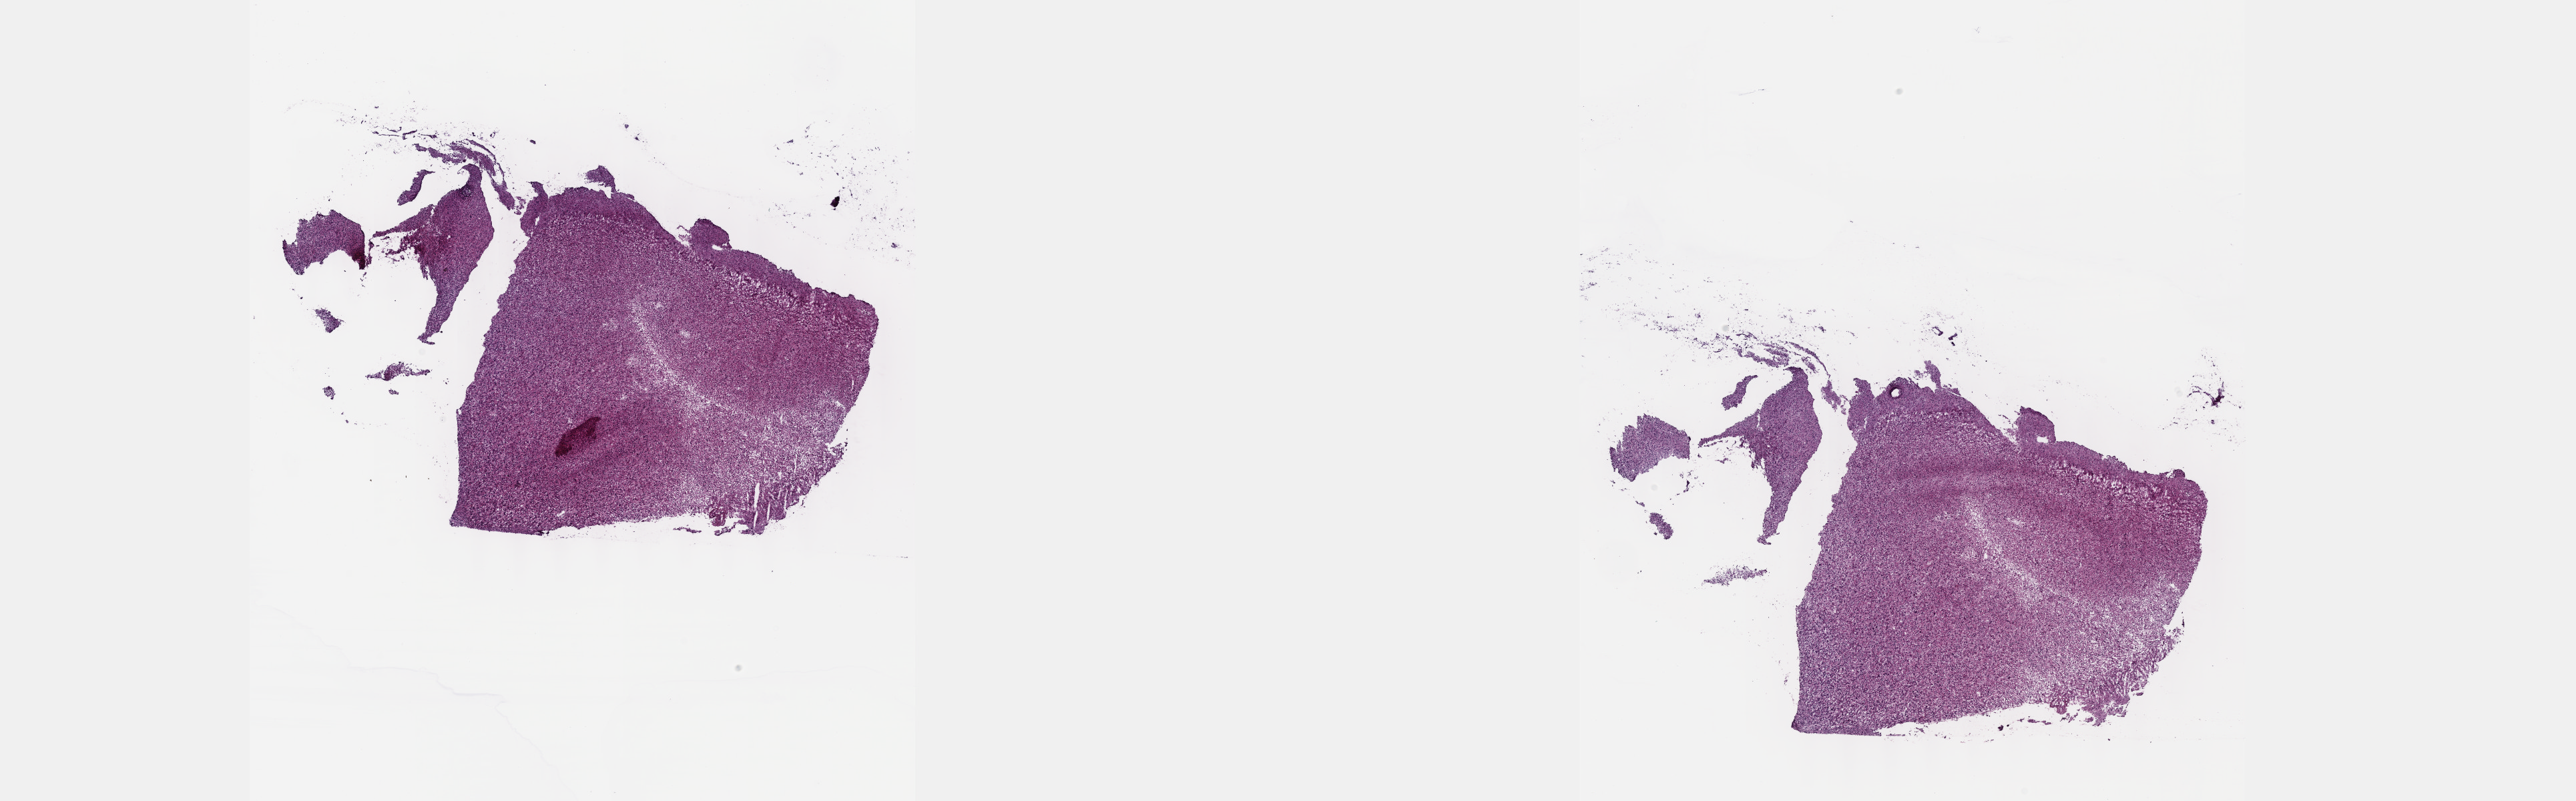
Whole-slide histology image, H&E-stained — shown as a low-resolution overview of the whole scanned area (about 31.2 x 9.7 mm, slide scanned at 40x), frozen section from the top of the tissue portion, sample: primary tumour, brain. Patient: male, age at initial diagnosis 55 years. Composition of this section per pathologist review: tumour cells 50%, tumour nuclei 90%.
Pathologic diagnosis: Astrocytoma, anaplastic (cerebrum).